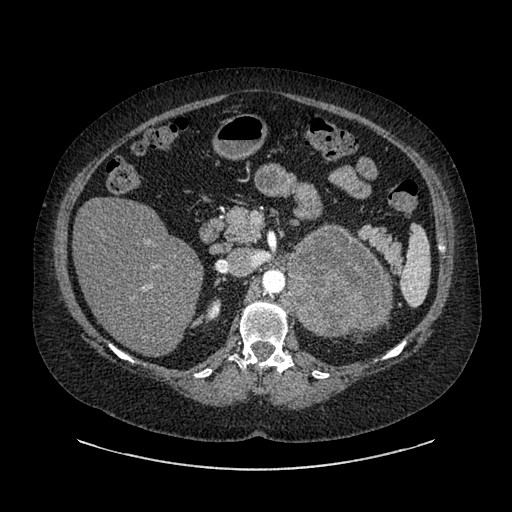
Contrast-enhanced abdominal CT, one axial slice; position 555 of 769 along the scan axis; reconstruction kernel SOFT; intravenous contrast given; soft-tissue window (W 400 / L 40 HU); 0.62 mm slice thickness; 512 × 512 image matrix, field of view 460 × 460 mm. Female patient, age 61 years. Case-level facts recorded for this patient, not image findings: diagnosis: adrenocortical carcinoma; tumour side: left adrenal; tumour size at pathology: 13 cm; Ki-67 index: 79 %; stage (as recorded): 2.
Annotated regions visible in this slice (semi-automatically segmented with operator editing):
- mass: bounding box [x1, y1, x2, y2] px = [290, 228, 390, 335]